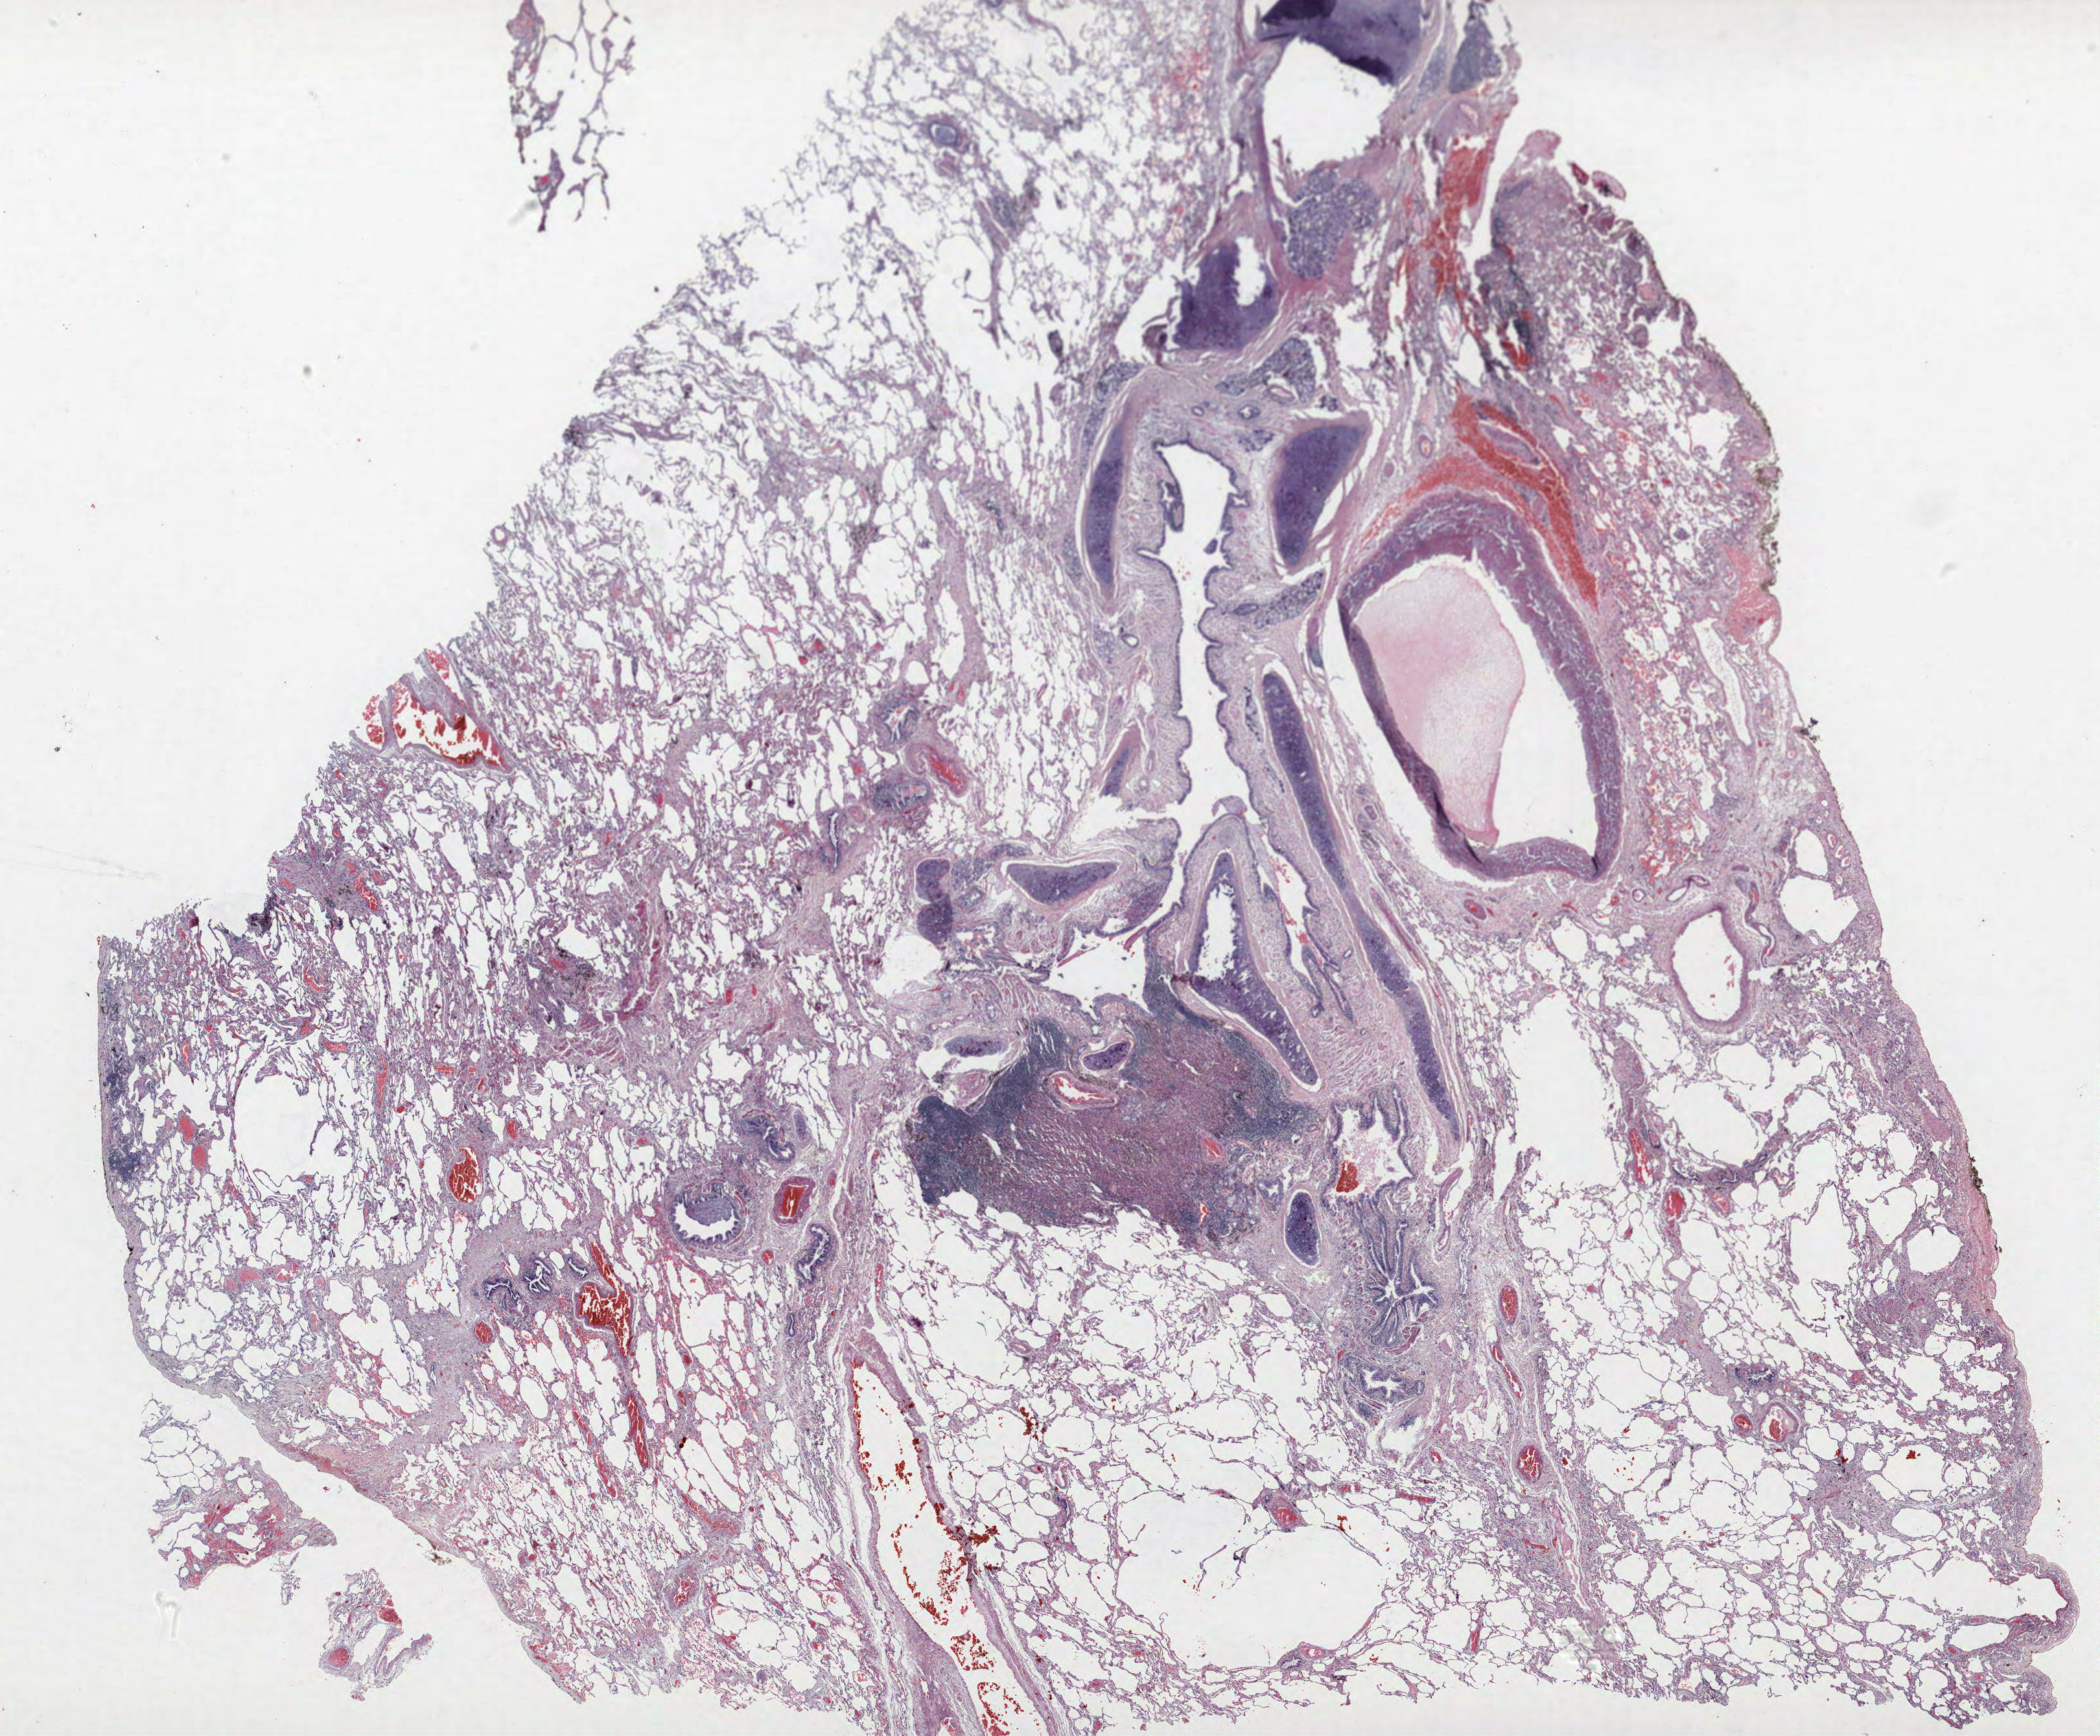
Whole-slide histology image, Hematoxylin and eosin (H&E) stained — shown as a low-resolution overview of the whole scanned area (about 25.9 x 21.4 mm, from a 40x scan), formalin-fixed paraffin-embedded (FFPE) section, lung. Female patient, aged 71 at enrolment. Former smoker at enrolment. Grade: poorly differentiated (G3).
Primary tumour location (clinical record): right upper lobe. Stage (AJCC 6th edition): IA. Participant's lung-cancer diagnosis: Squamous cell carcinoma, NOS (ICD-O-3 8070/3). Tumour size (pathology): 30 mm.